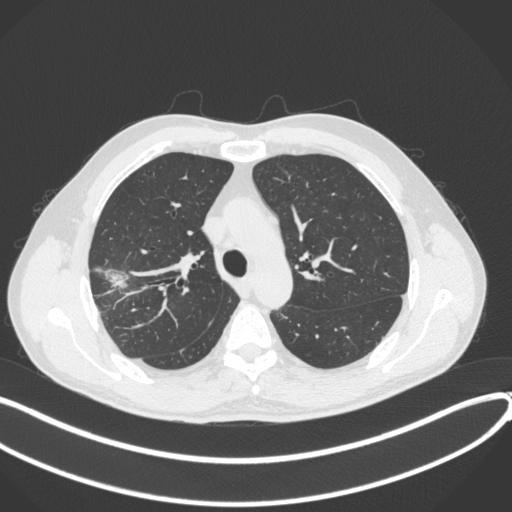
Chest CT, one axial slice. Slice 299 of 381 in the series (ordered by position). Reconstruction kernel B31f. 120 kVp. Lung window (W 1500 / L -600 HU). 512 × 512 image matrix, field of view 400 × 400 mm. Male patient, age 62 years. From the clinical record (not read from this slice): clinical TNM (as recorded): T1c N0 M0.
Structures marked on this image (rectangle marked by the reading radiologist):
- lung tumour (recorded histology: adenocarcinoma): bounding box (x1, y1, x2, y2) in pixels: (96, 263, 128, 292)